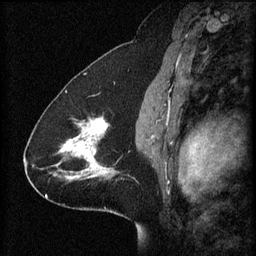
Breast MRI (dynamic contrast-enhanced), one sagittal slice; slice 38 of 60 in the series (ordered by position); 3 images stored at this slice position (order not interpretable as contrast timing); 1.5 T; TE 4.2 ms, TR 8.2 ms; 256 × 256 image matrix, field of view 200 × 200 mm. Female patient, age 41 years.
Outlined on this slice (semi-automatic segmentation, software-assisted and operator-edited):
- analysis volume of interest (the breast-tissue region the enhancement analysis was run in; not a lesion): bounding box <58,118,120,181> (left, top, right, bottom; pixels)
- tumour enhancement mask (voxels above the 70 % enhancement threshold inside the analysis volume of interest): <61,118,115,179>